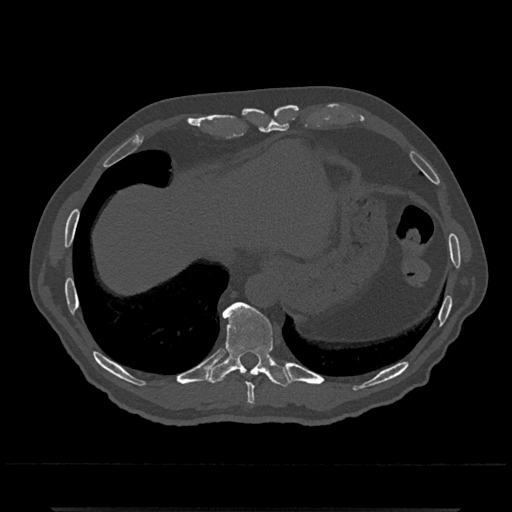
CT including the spine, one axial slice. Position 570 of 797 along the scan axis. Reconstruction kernel Br40s/3. Bone window (W 1800 / L 400 HU). 0.5 mm slice thickness. 512 × 512 image matrix, field of view 393 × 393 mm. Male patient, age 67 years. Case-level facts recorded for this patient, not image findings: primary cancer: prostate.
Outlined on this slice (semi-automatically segmented with operator editing):
- T10 vertebra: bounding box (x1, y1, x2, y2) in pixels: (206, 302, 292, 387)
- T9 vertebra: (247, 383, 255, 405)